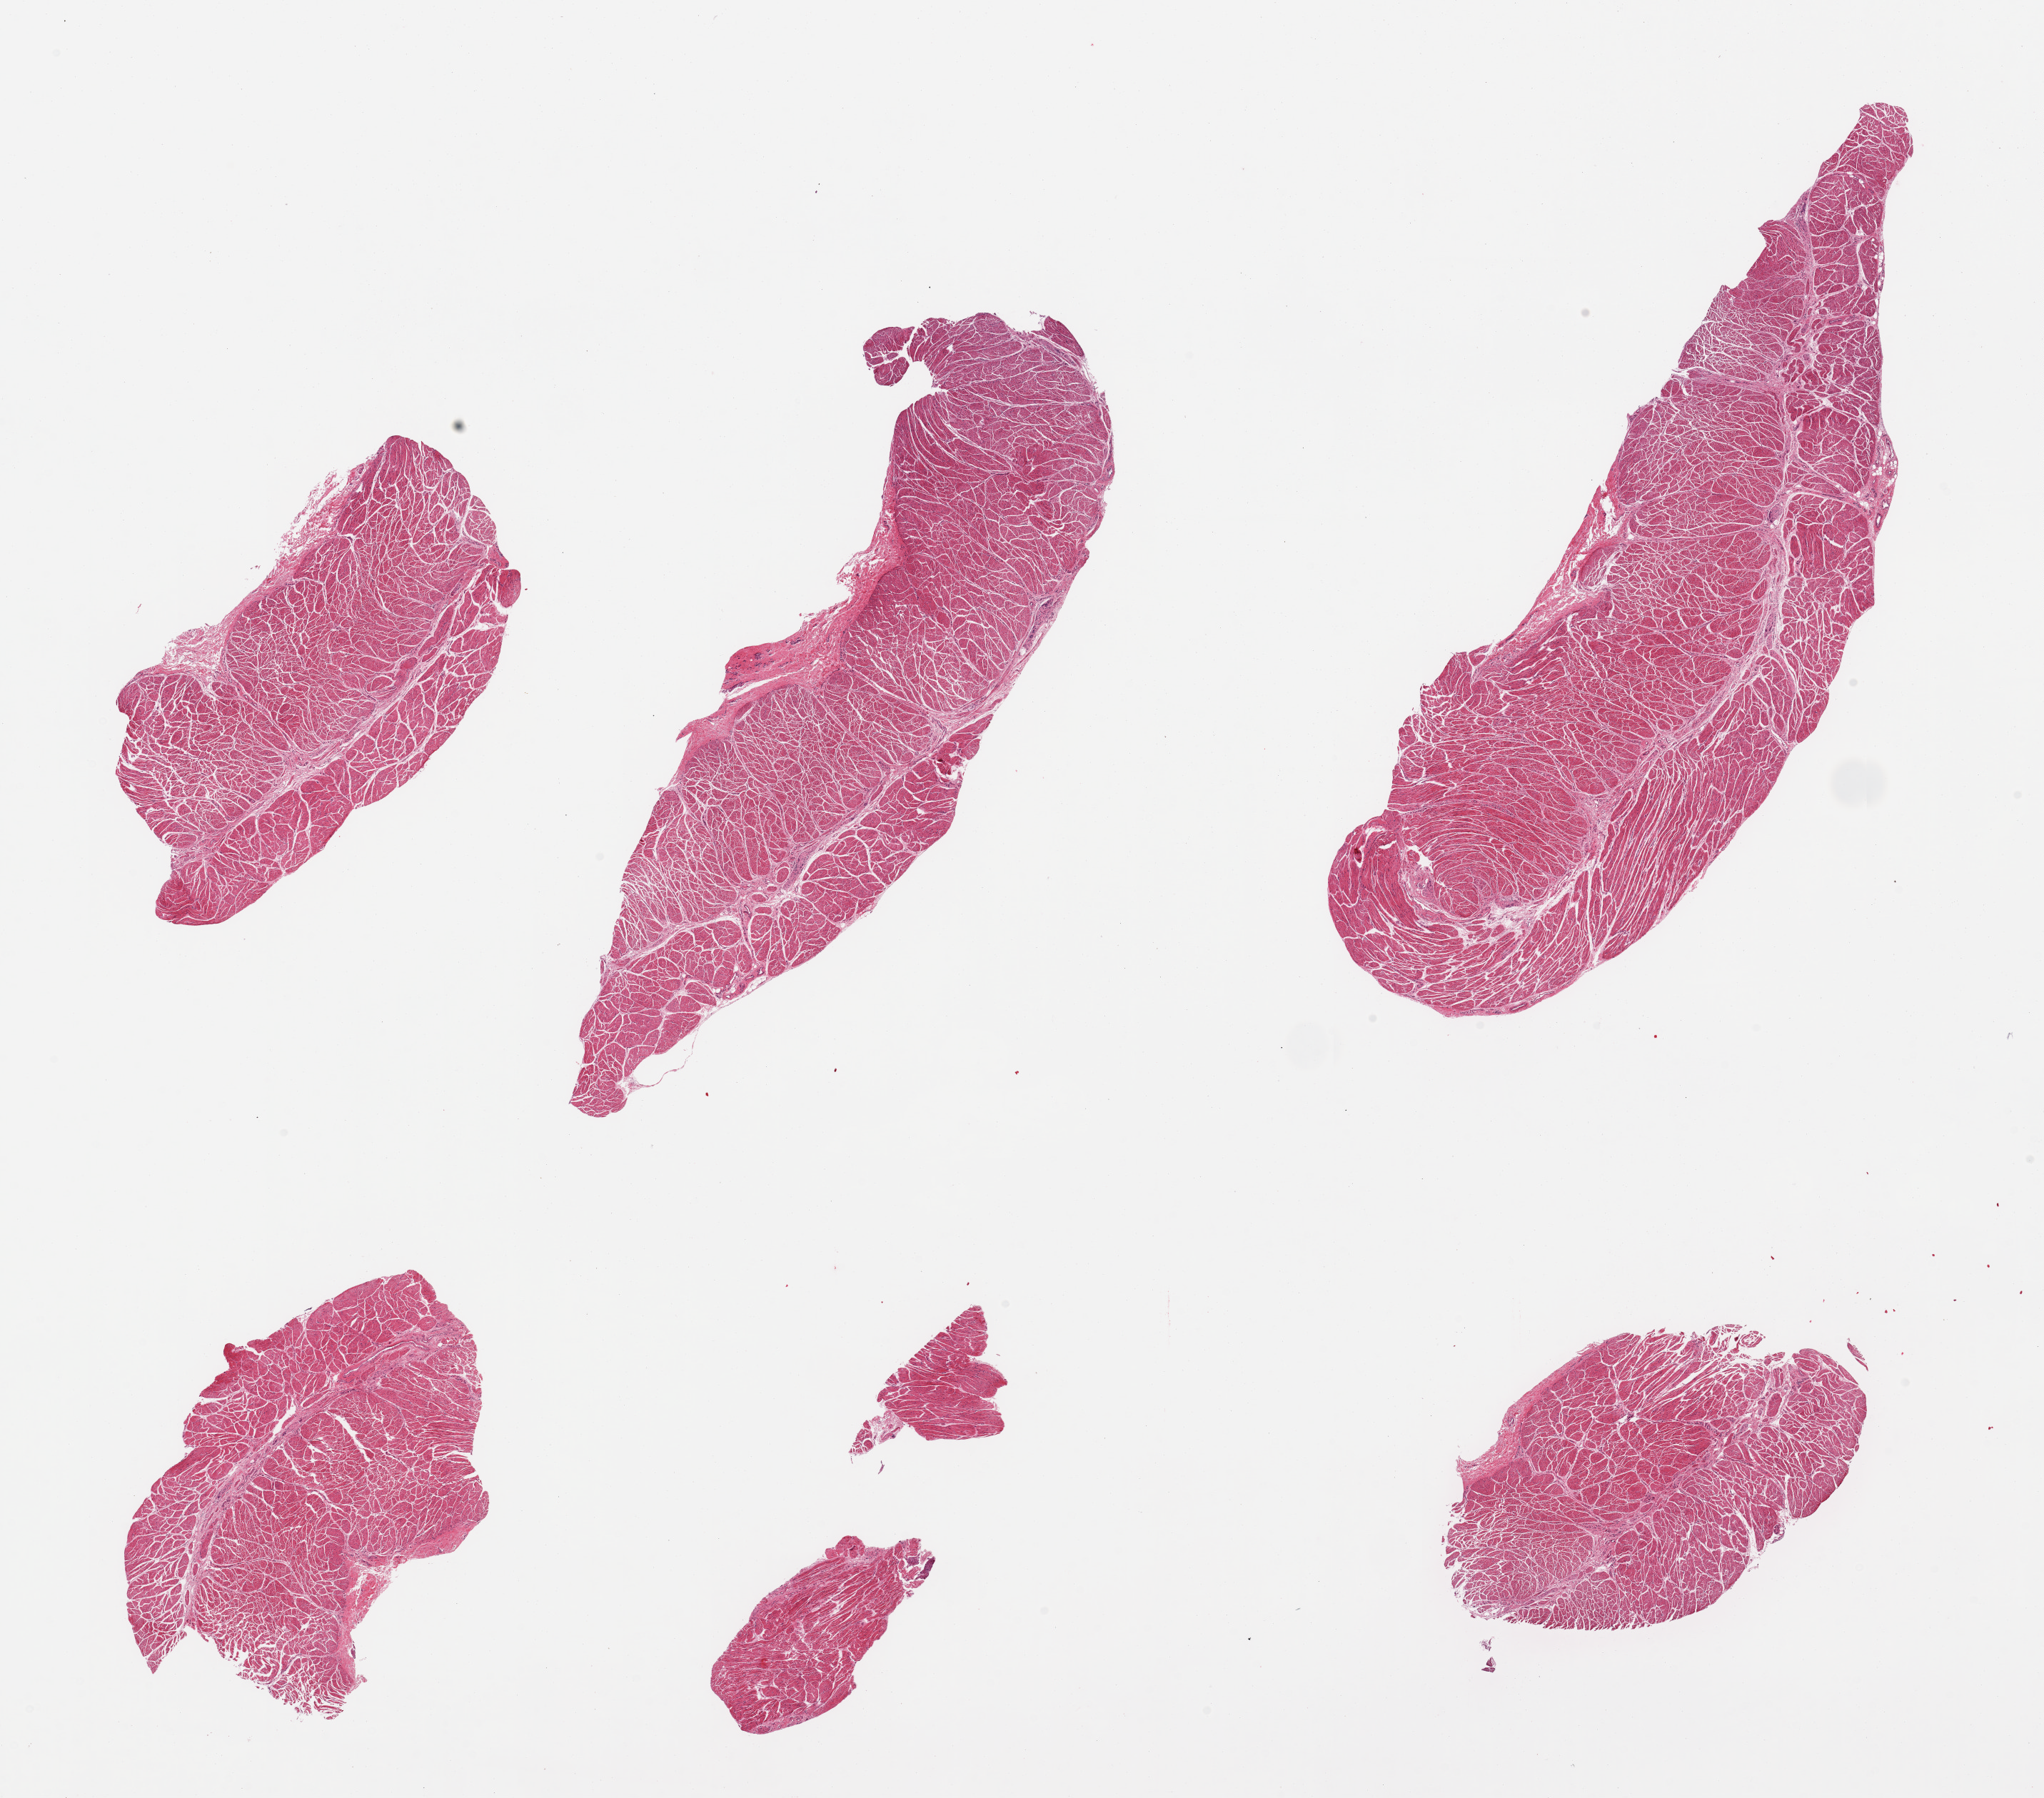
Whole-slide image, hematoxylin and eosin (H&E) stain, brightfield — shown as a low-resolution overview of the whole scanned area (about 22.6 x 19.9 mm, acquisition: 20x scan), PAXgene-fixed paraffin-embedded (PFPE) section, sampled site (target tissue): esophageal muscle, donor tissue sample.
Pathologist's review note for this sample: 6 pieces (one of them fragmented); well trimmed.